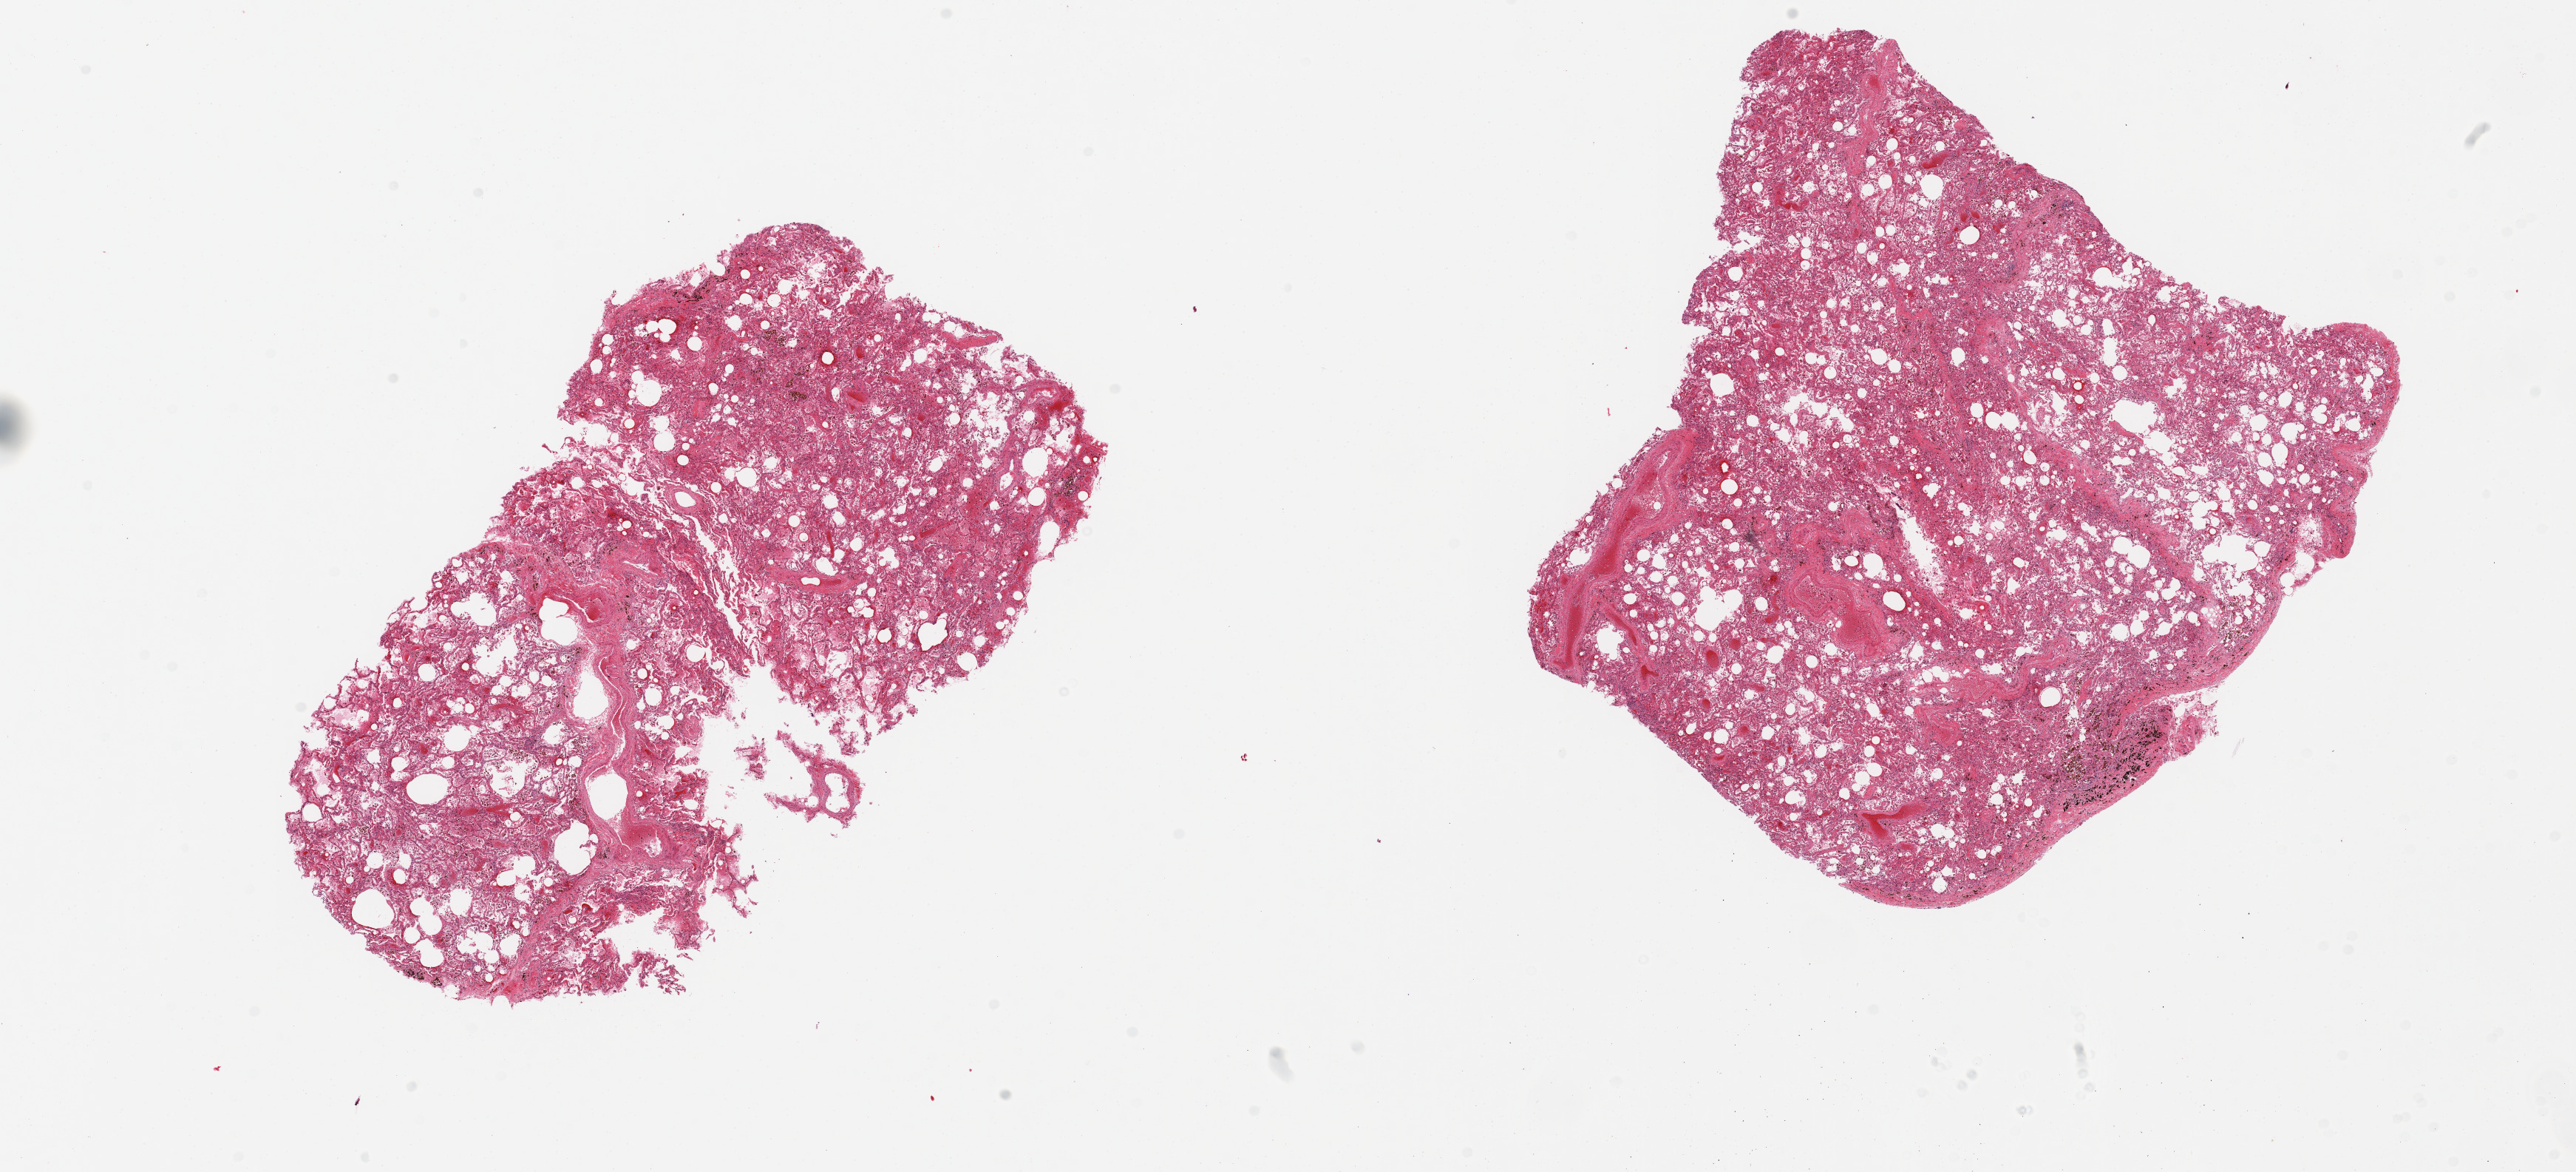
Whole-slide image, H&E stain, low-resolution overview of the scanned area, about 27.6 x 12.5 mm (acquisition: 20x scan), PAXgene-fixed paraffin-embedded (PFPE) section, target tissue: lung, tissue donor sample. Male donor.
Review note (as recorded): 2 pieces, moderate congestion/edema.